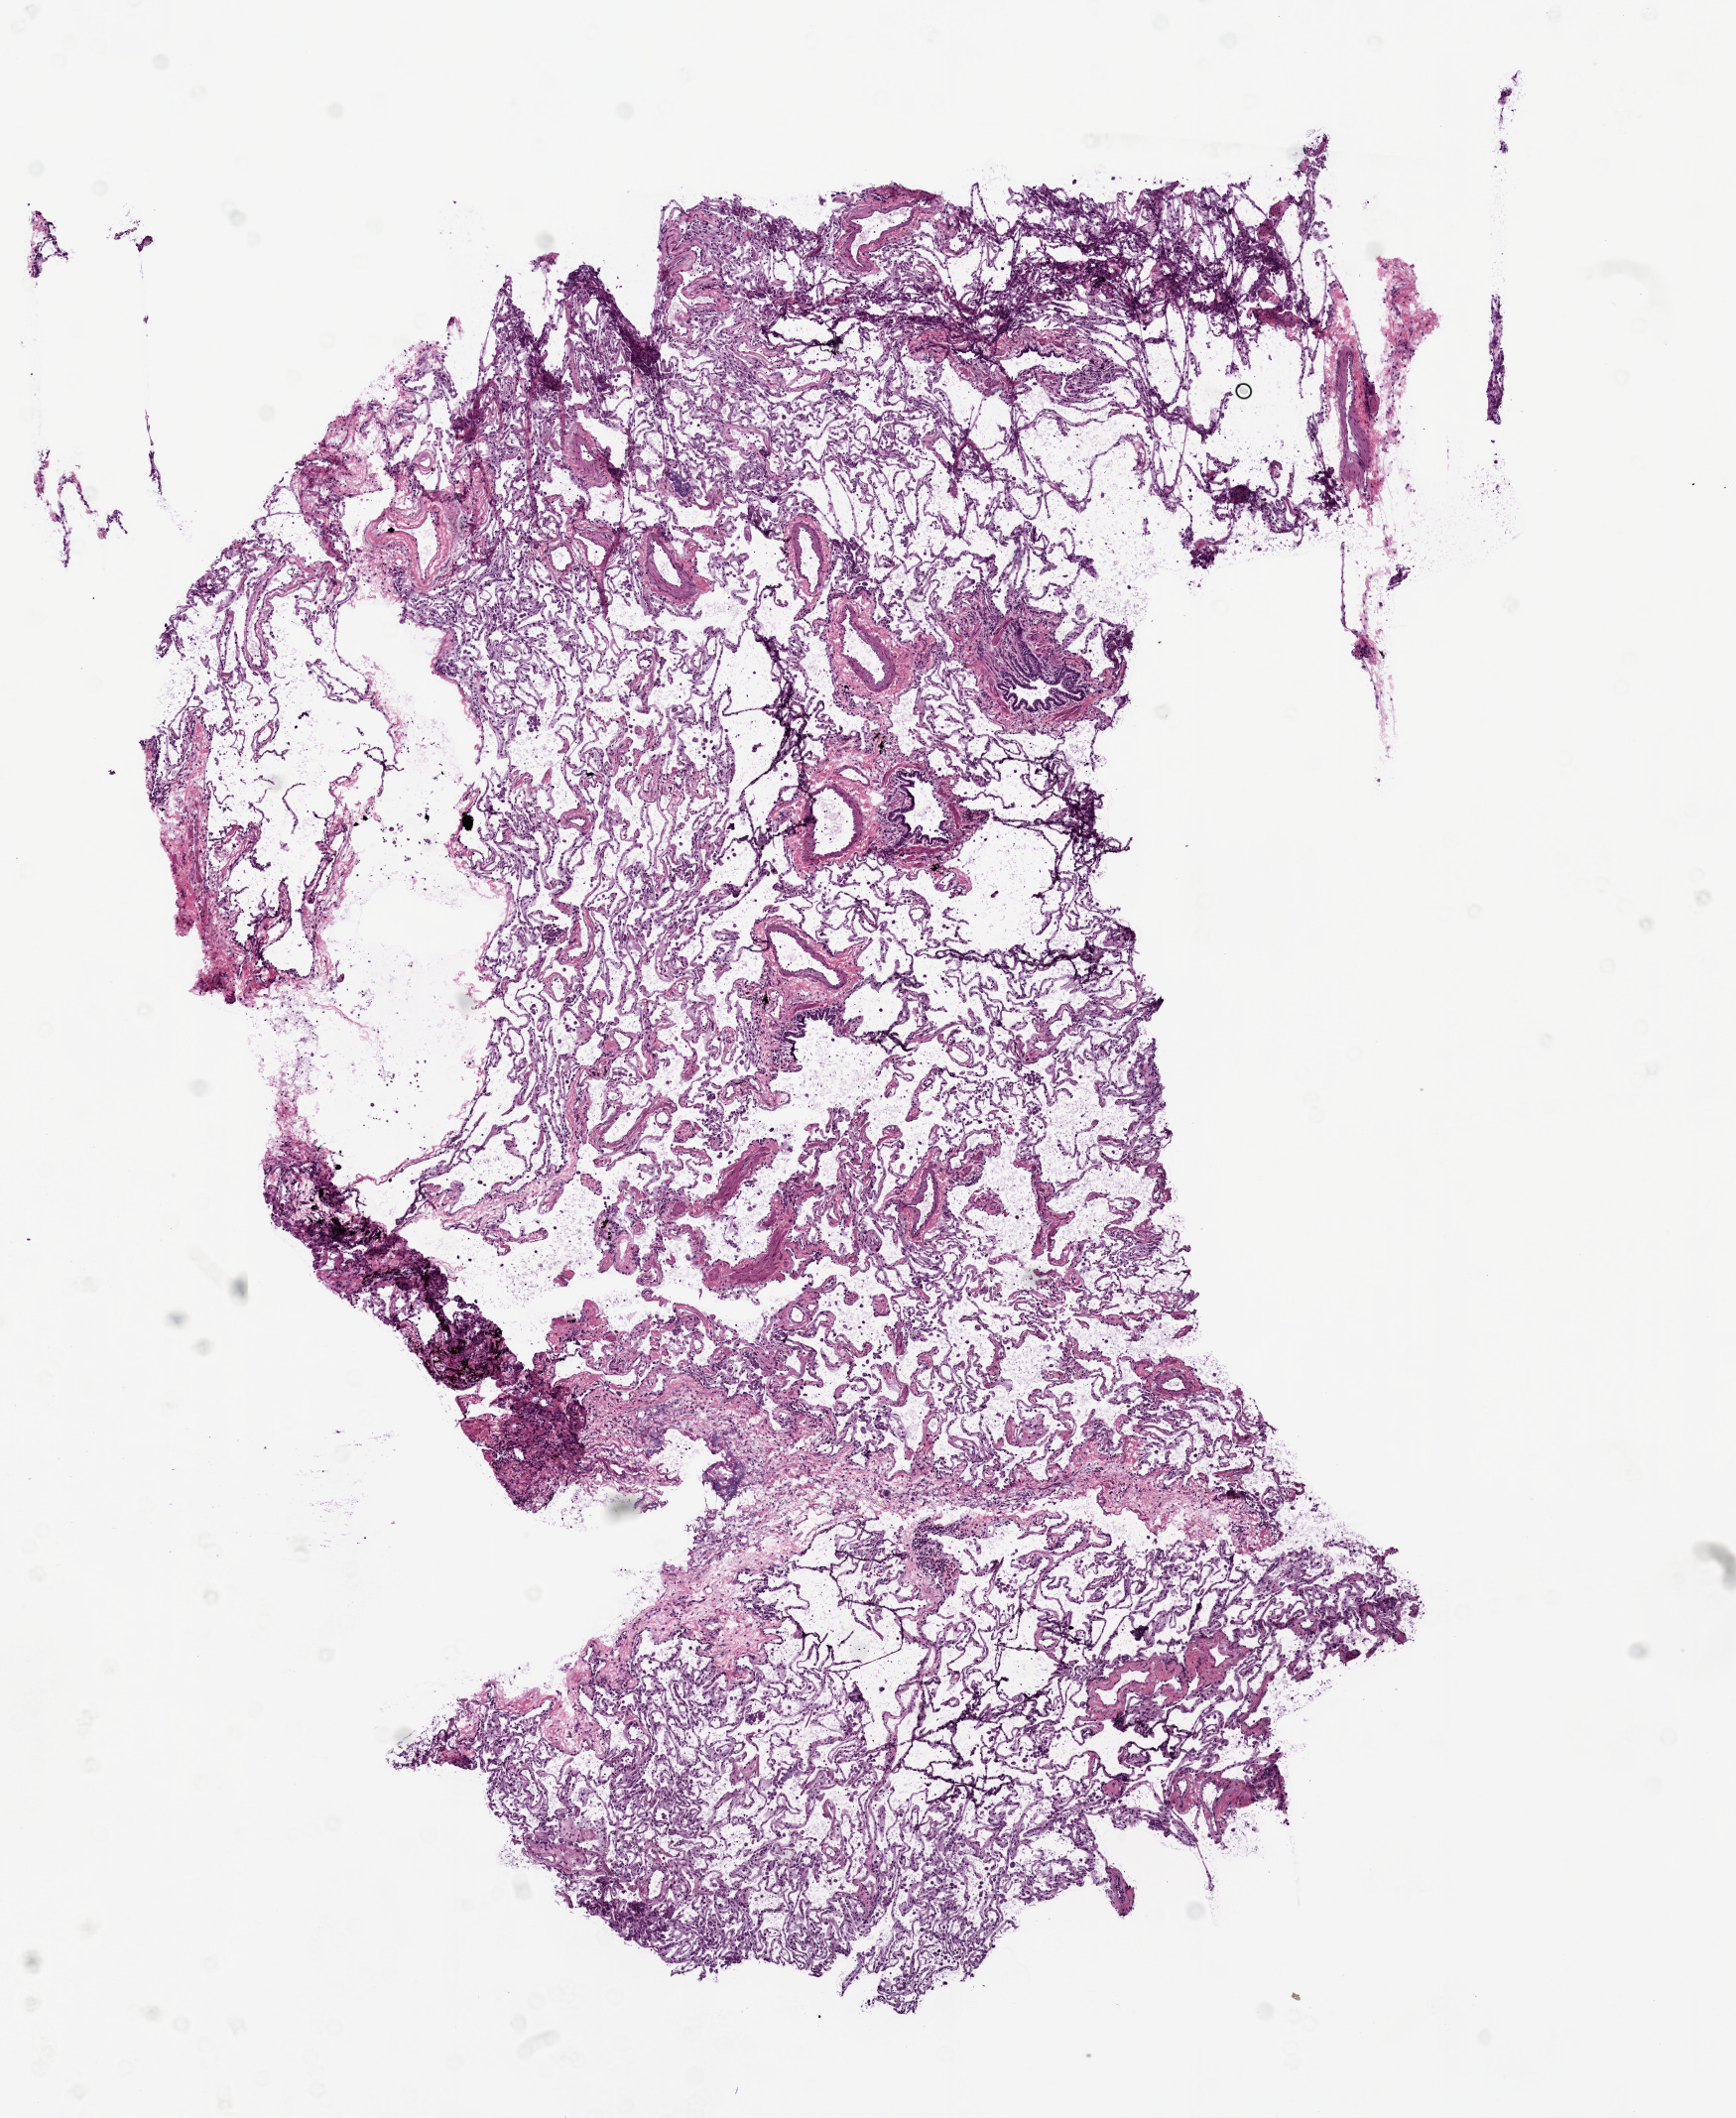
Whole-slide histology image, Hematoxylin and eosin (H&E) stained, low-resolution overview of the scanned area, about 7.0 x 8.6 mm. Frozen section from the top of the tissue portion. Lung, solid tissue normal (non-tumour tissue) sample. Patient: male, age at initial diagnosis 73 years.
This section: solid tissue normal (non-tumour) sample from the same patient. Patient diagnosis: Squamous cell carcinoma, NOS.